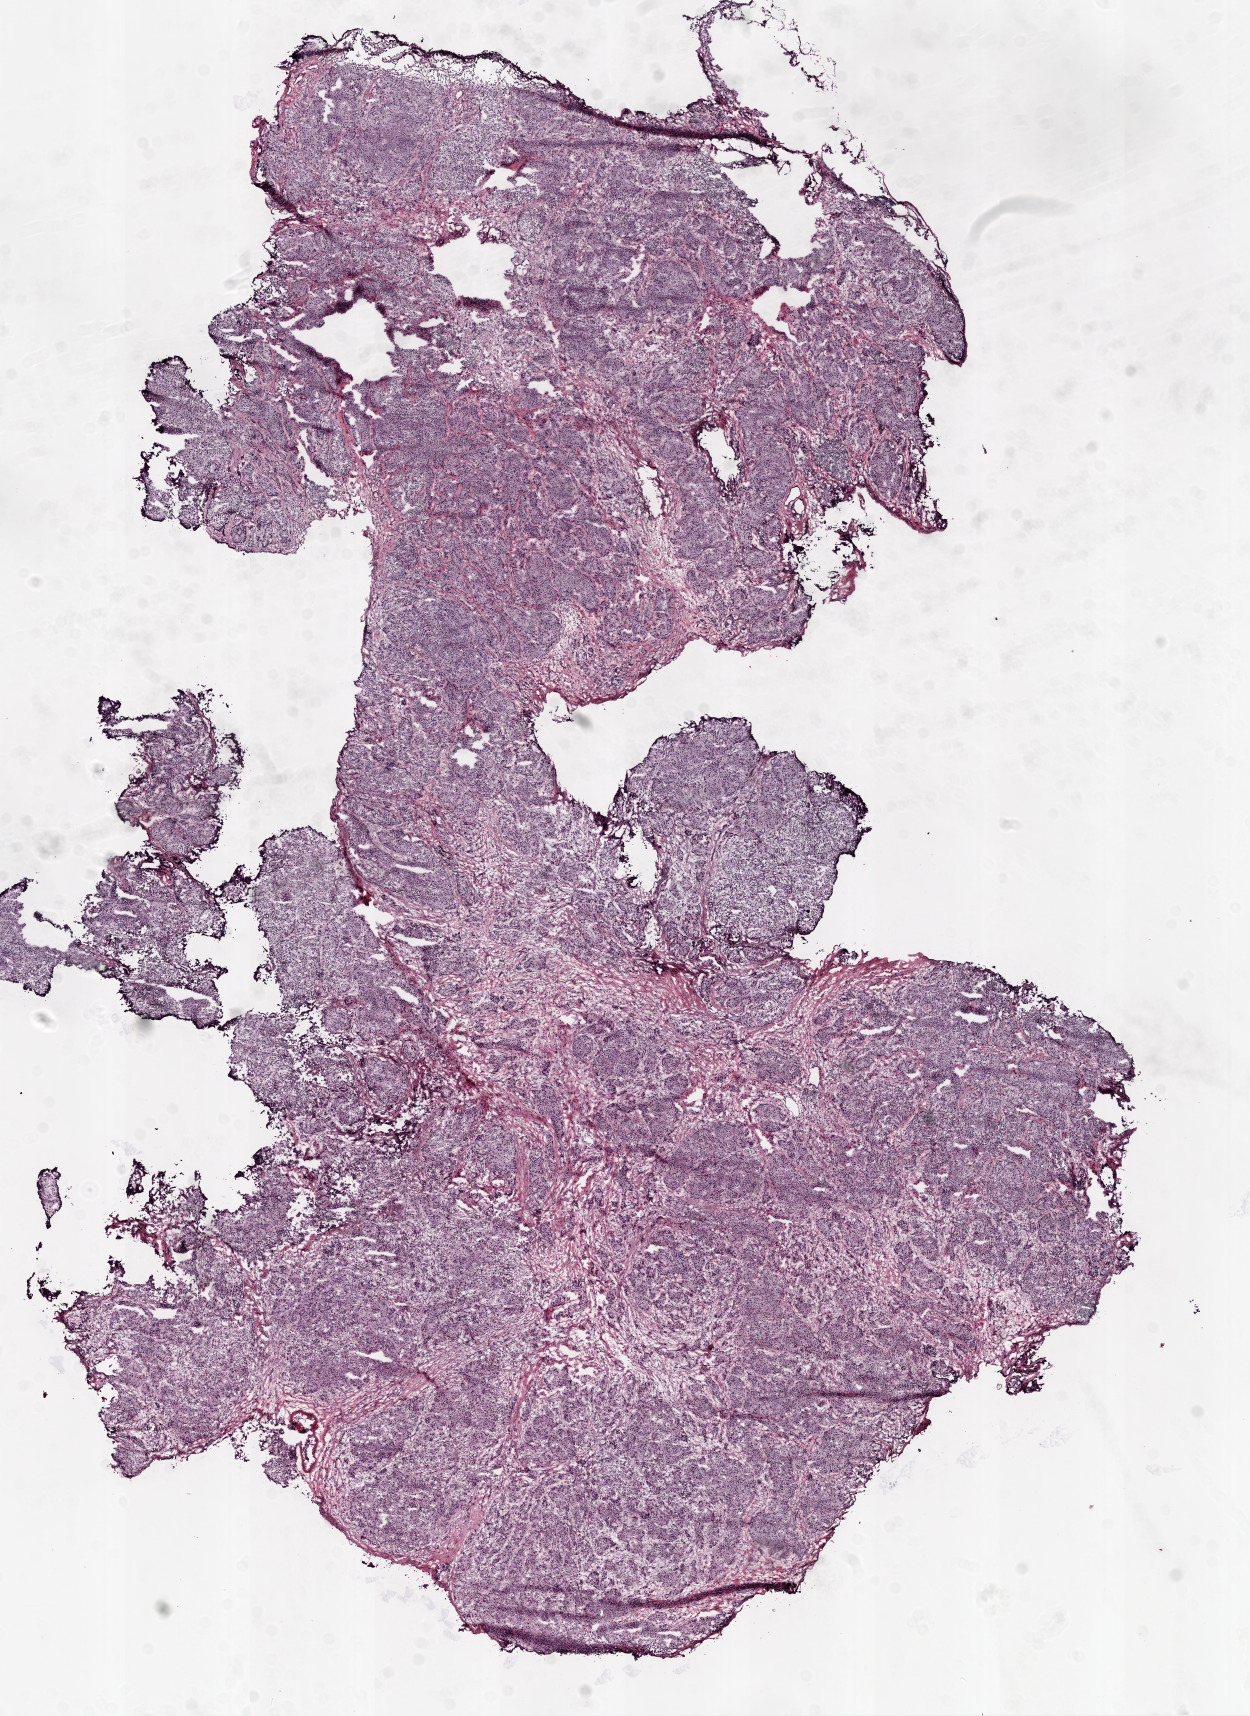
H&E whole-slide image, shown as a low-resolution overview of the whole scanned area (about 10.0 x 13.8 mm, from a 20x scan); frozen section from the top of the tissue portion; sample: primary tumour, ovary. Patient: female, age at initial diagnosis 60 years. Histologic grade: G3 (poorly differentiated). Pathologist review of this section (percent, as recorded): tumour cells 80%, tumour nuclei 90%, normal cells 0%, stromal cells 15%, necrosis 5%.
- pathologic diagnosis: Serous cystadenocarcinoma, NOS
- laterality: left
- FIGO stage: IIIC